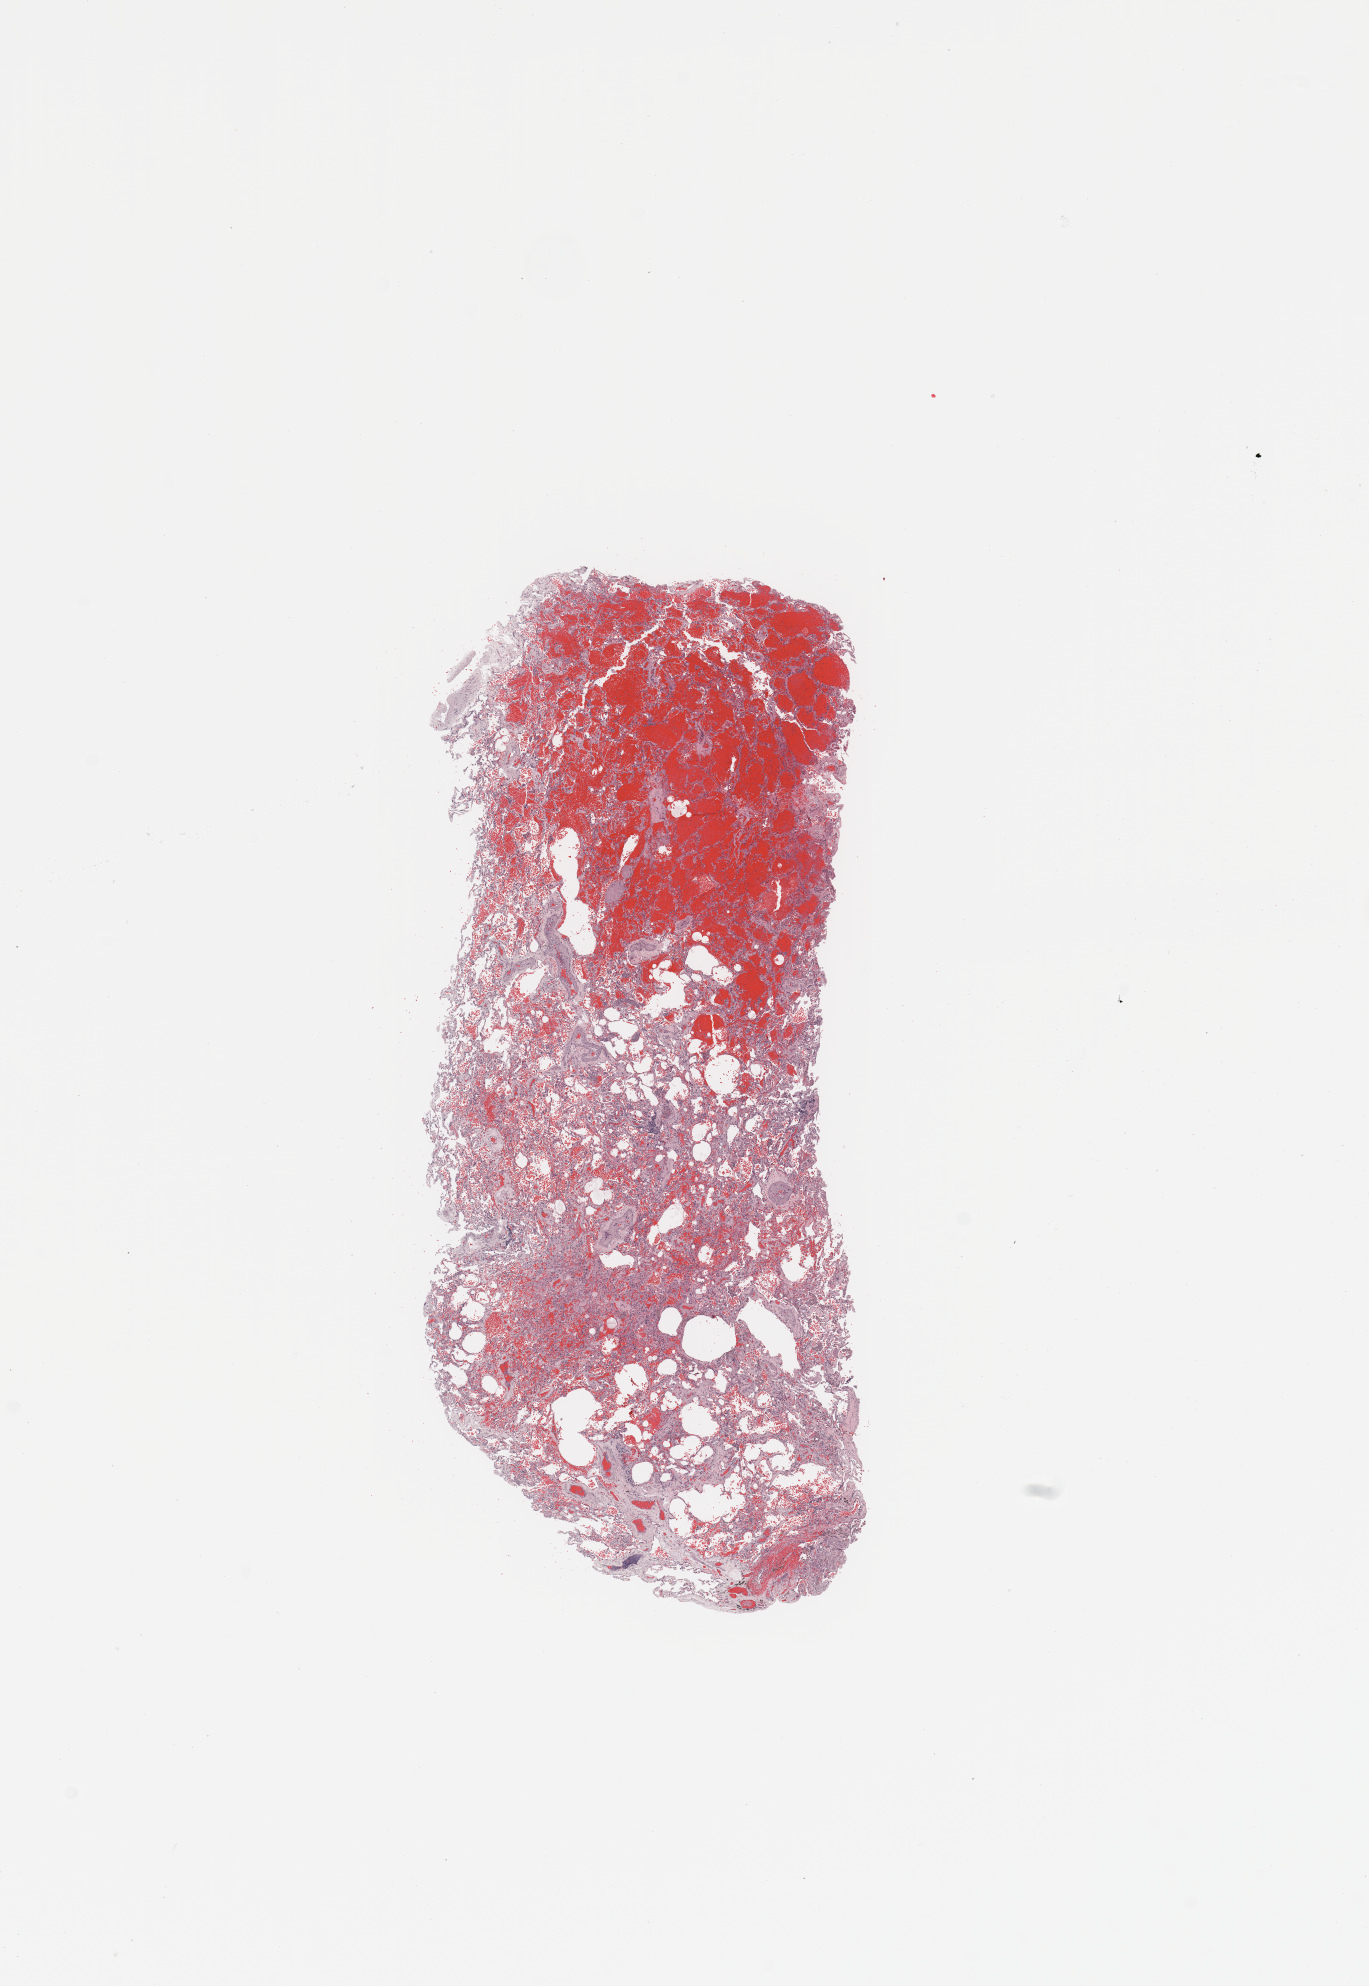
Digitized H&E tissue section (whole slide), a low-resolution overview of the entire scanned area, about 10.8 x 15.7 mm (from a 20x scan), lung, normal (non-tumour) tissue. Patient: female, age 66 years.
This section: normal (non-tumour) tissue from the same patient. Patient diagnosis: Adenocarcinoma, NOS.